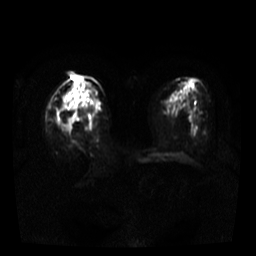
Breast MRI, one axial slice. Position 16 of 37 along the scan axis. Diffusion-weighted series; image 2 of 4 stored at this slice position (different b-values; order by instance number). 3 T. 5 mm slice thickness. 256 × 256 image matrix, field of view 320 × 320 mm. Female patient.
Outlined on this slice (outlined manually by an expert reader):
- tumour on diffusion-weighted imaging: bounding box [x1, y1, x2, y2] px = [64, 118, 73, 131]